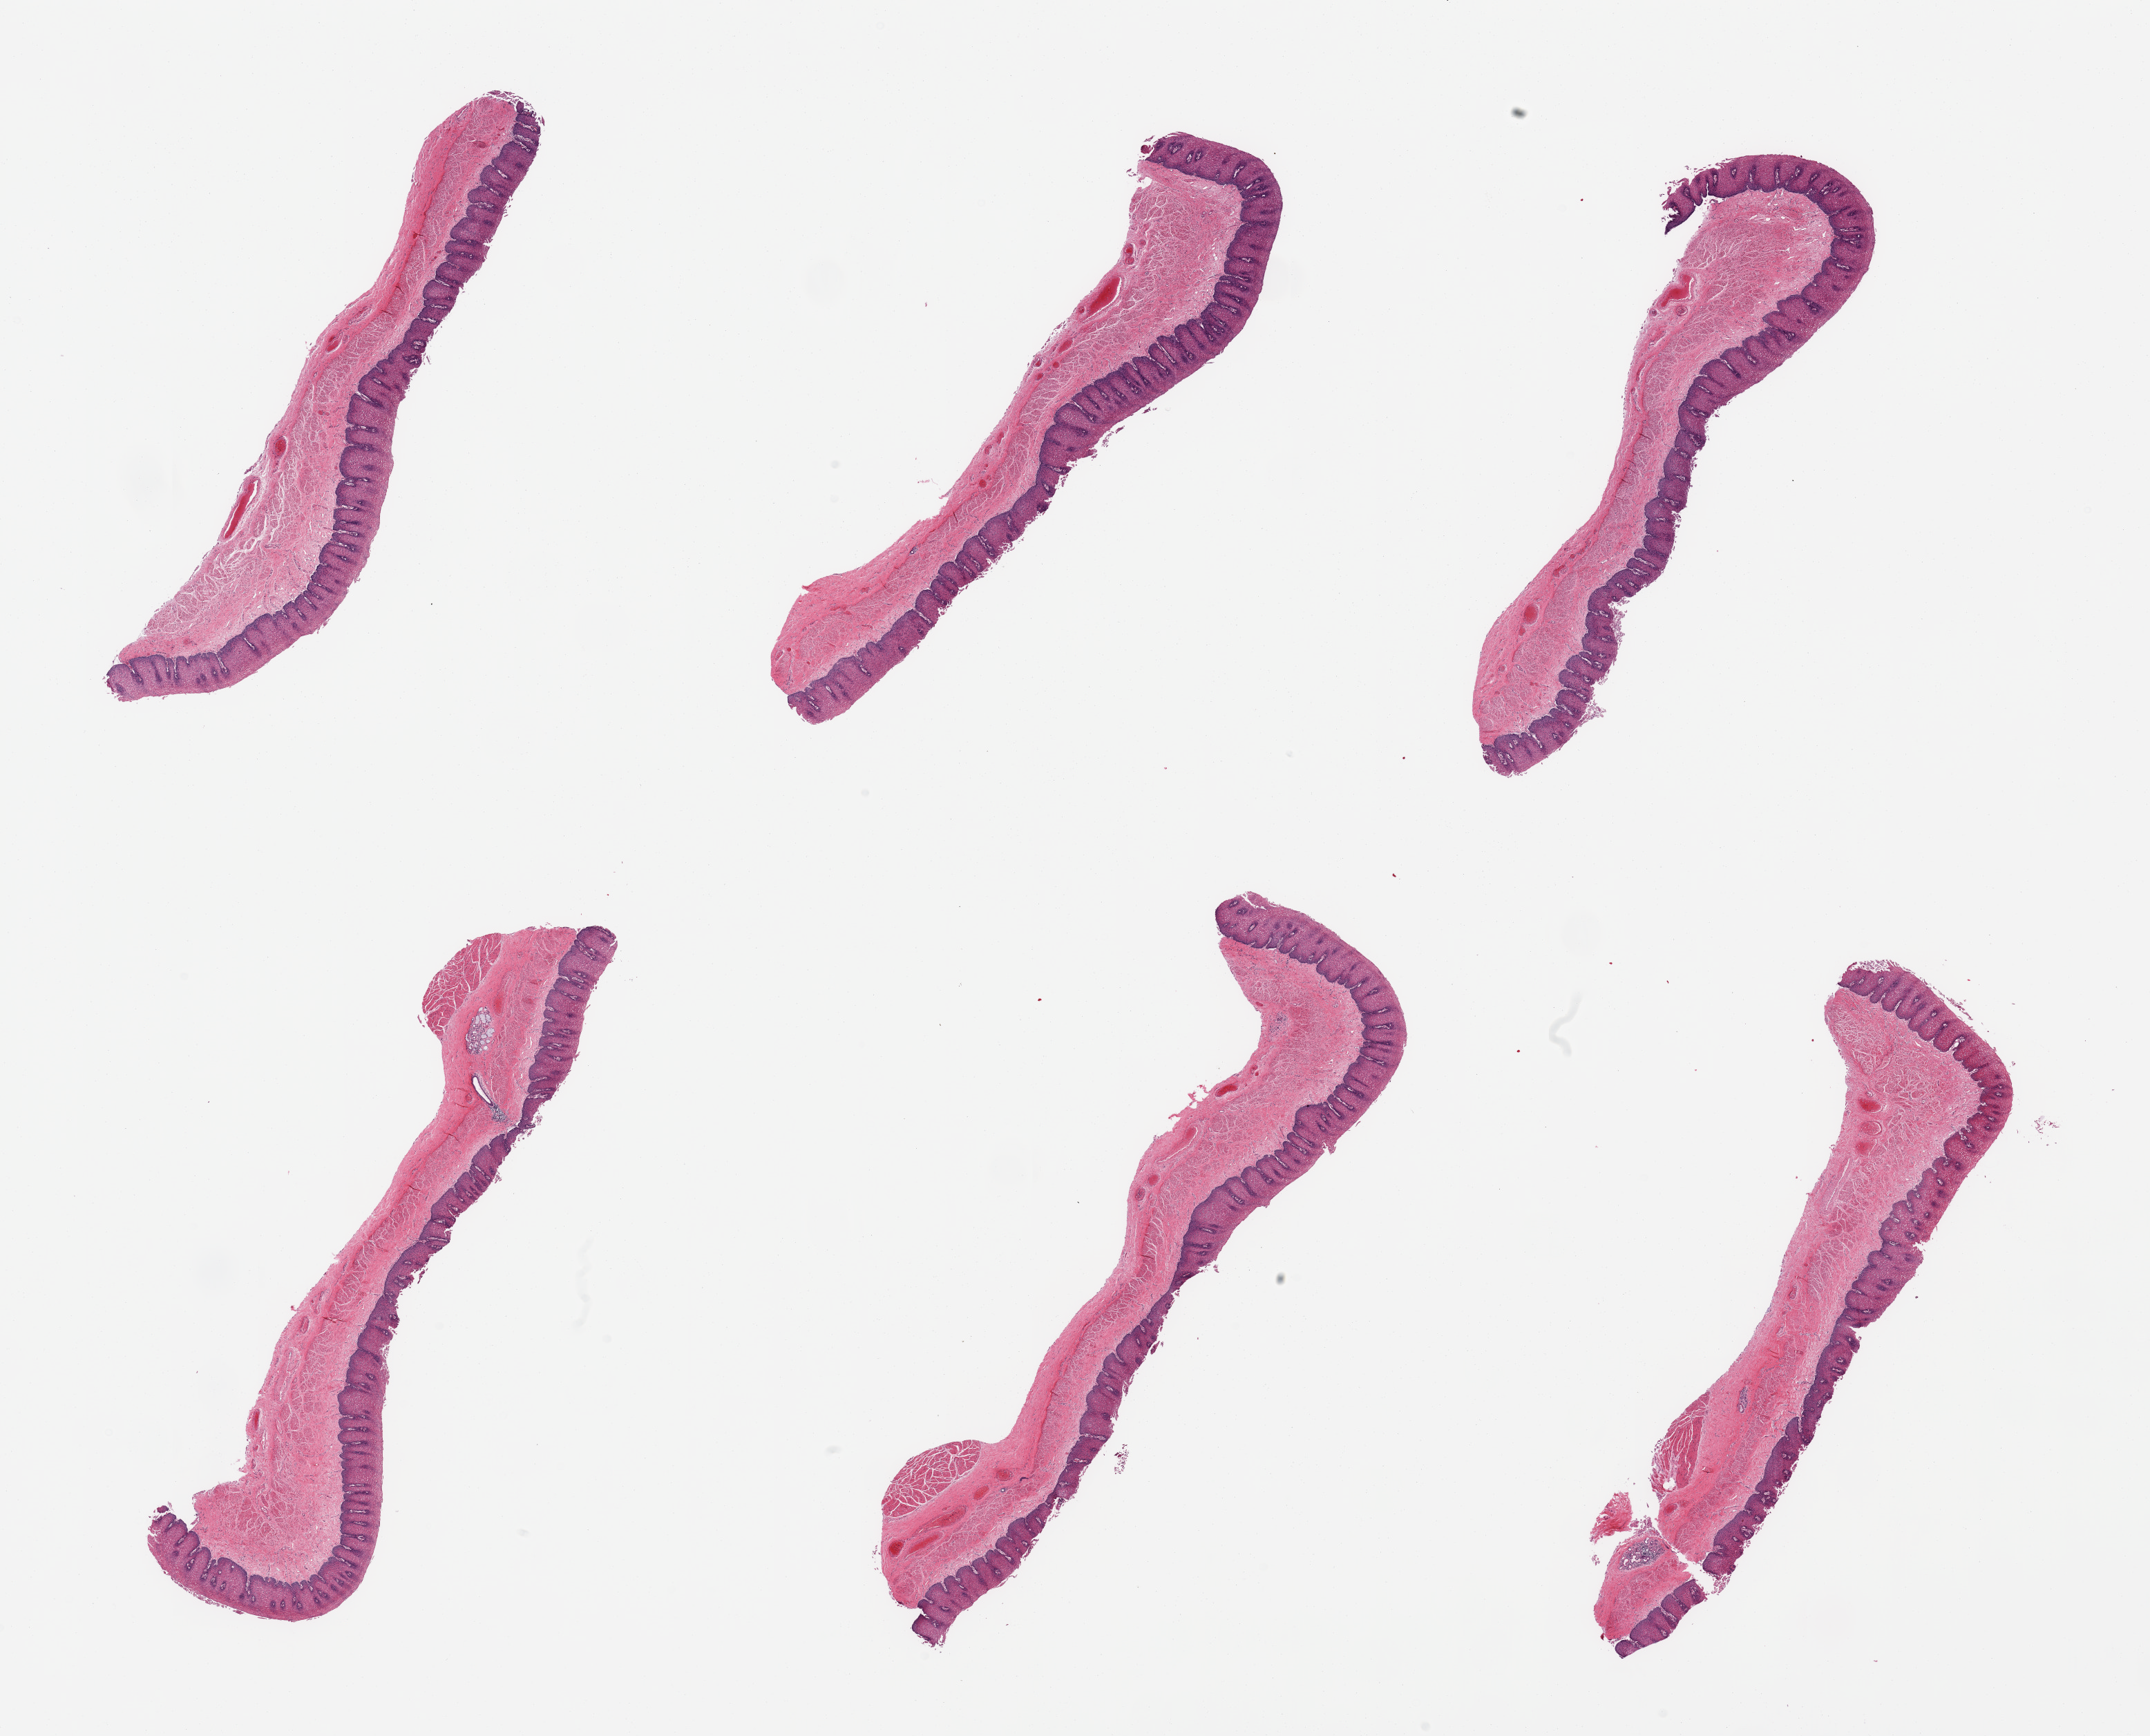
Digitized hematoxylin and eosin (H&E)-stained section — low-resolution overview of the scanned area, about 24.6 x 19.9 mm, PAXgene-fixed, paraffin-embedded tissue, target tissue: esophageal mucous membrane, donor tissue sample. Male donor.
• pathologist's review note for this sample: 6 pieces, squamous mucosa up to ~0.5mm, ~30% thickness